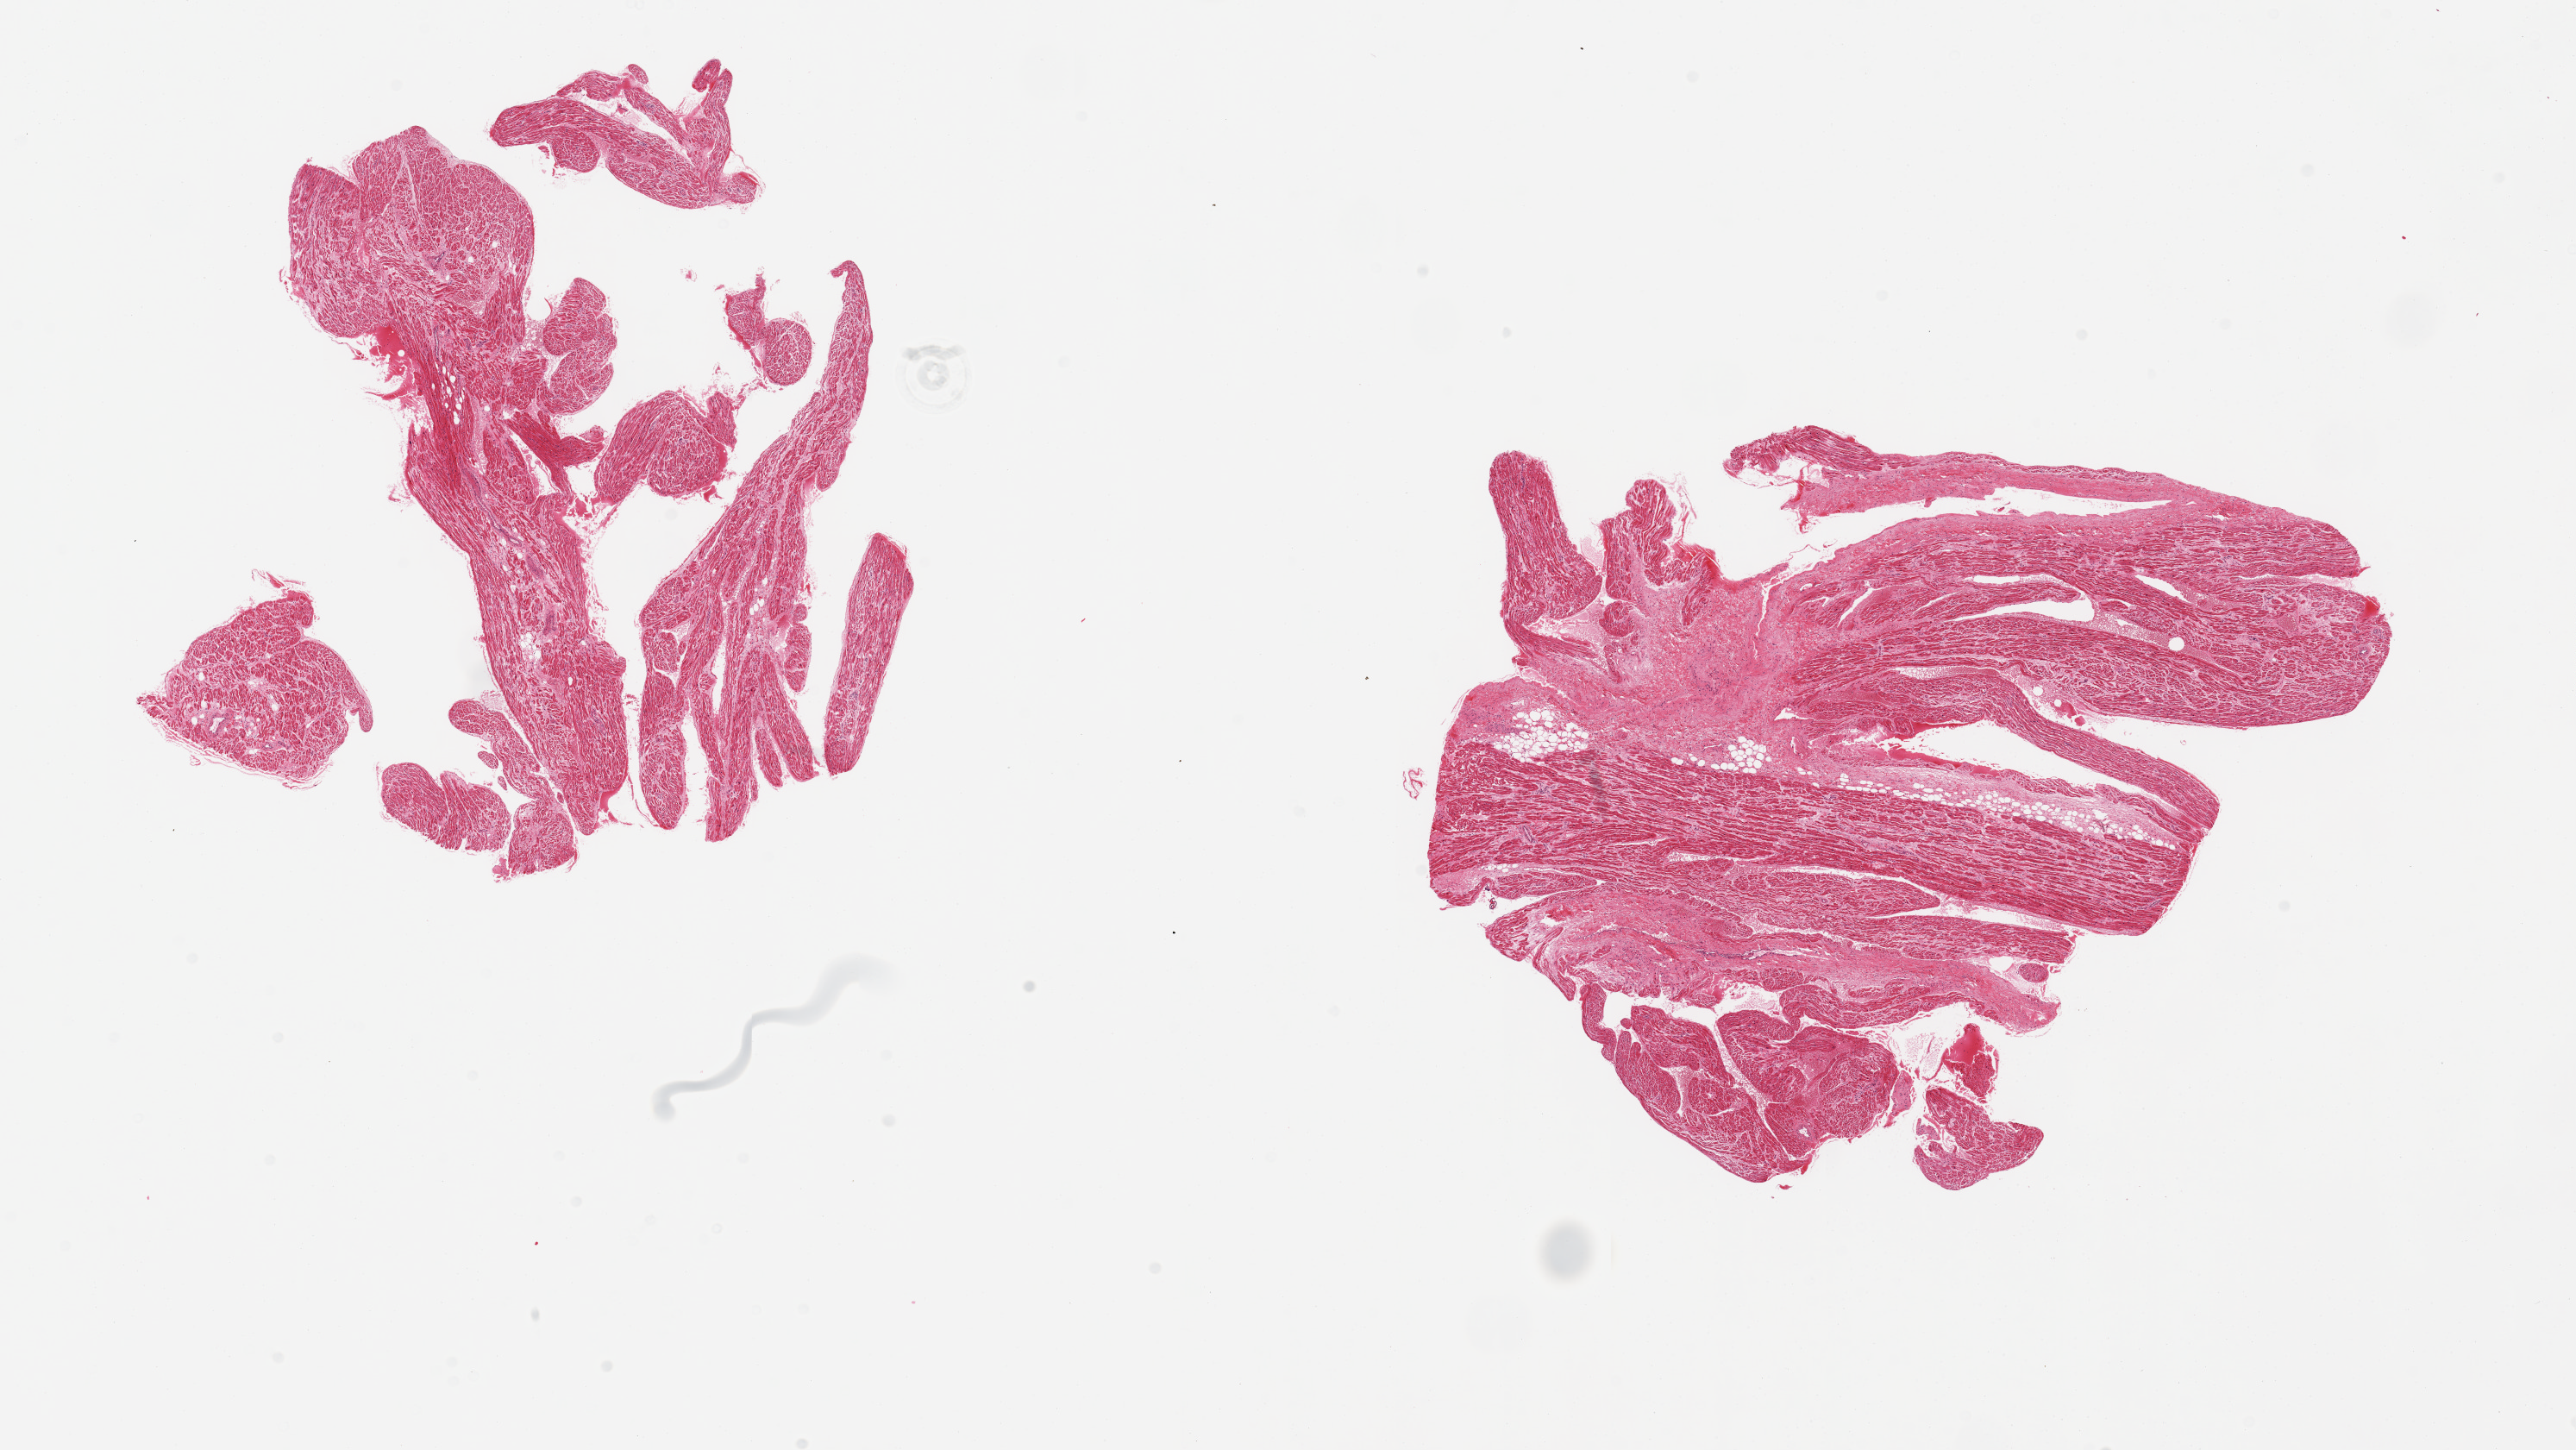
Digitized H&E-stained section — low-resolution overview of the scanned area, about 23.6 x 13.3 mm. PAXgene-fixed paraffin-embedded (PFPE) section. Section of auricular appendage (target tissue). Donor tissue sample.
Reviewer comment on this tissue sample: 2 pieces; 20% fibrofatty content in 1; hypereosinophilia (ischemic) in other.